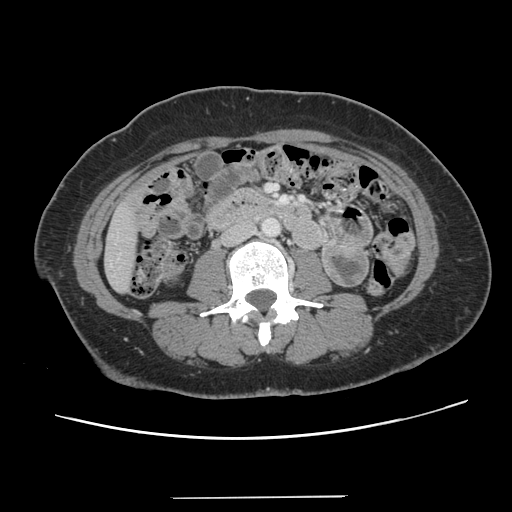
Contrast-enhanced abdominal CT, one axial slice; slice 26 of 141 in the series (ordered by position); 120 kVp; intravenous contrast given; soft-tissue window (W 400 / L 40 HU); 2.5 mm slice thickness; 512 × 512 image matrix, field of view 366 × 366 mm. Female patient, age 53 years. Case-level facts recorded for this patient, not image findings: diagnosis: colorectal cancer liver metastases, imaged before liver resection; multiple liver metastases: no; largest metastasis: 14.5 cm; chemotherapy before resection: yes.
Outlined on this slice (expert manual segmentation):
- liver: bounding box <106,203,138,291> (left, top, right, bottom; pixels)
- planned liver remnant (the part of the liver to remain after resection): <106,206,138,291>